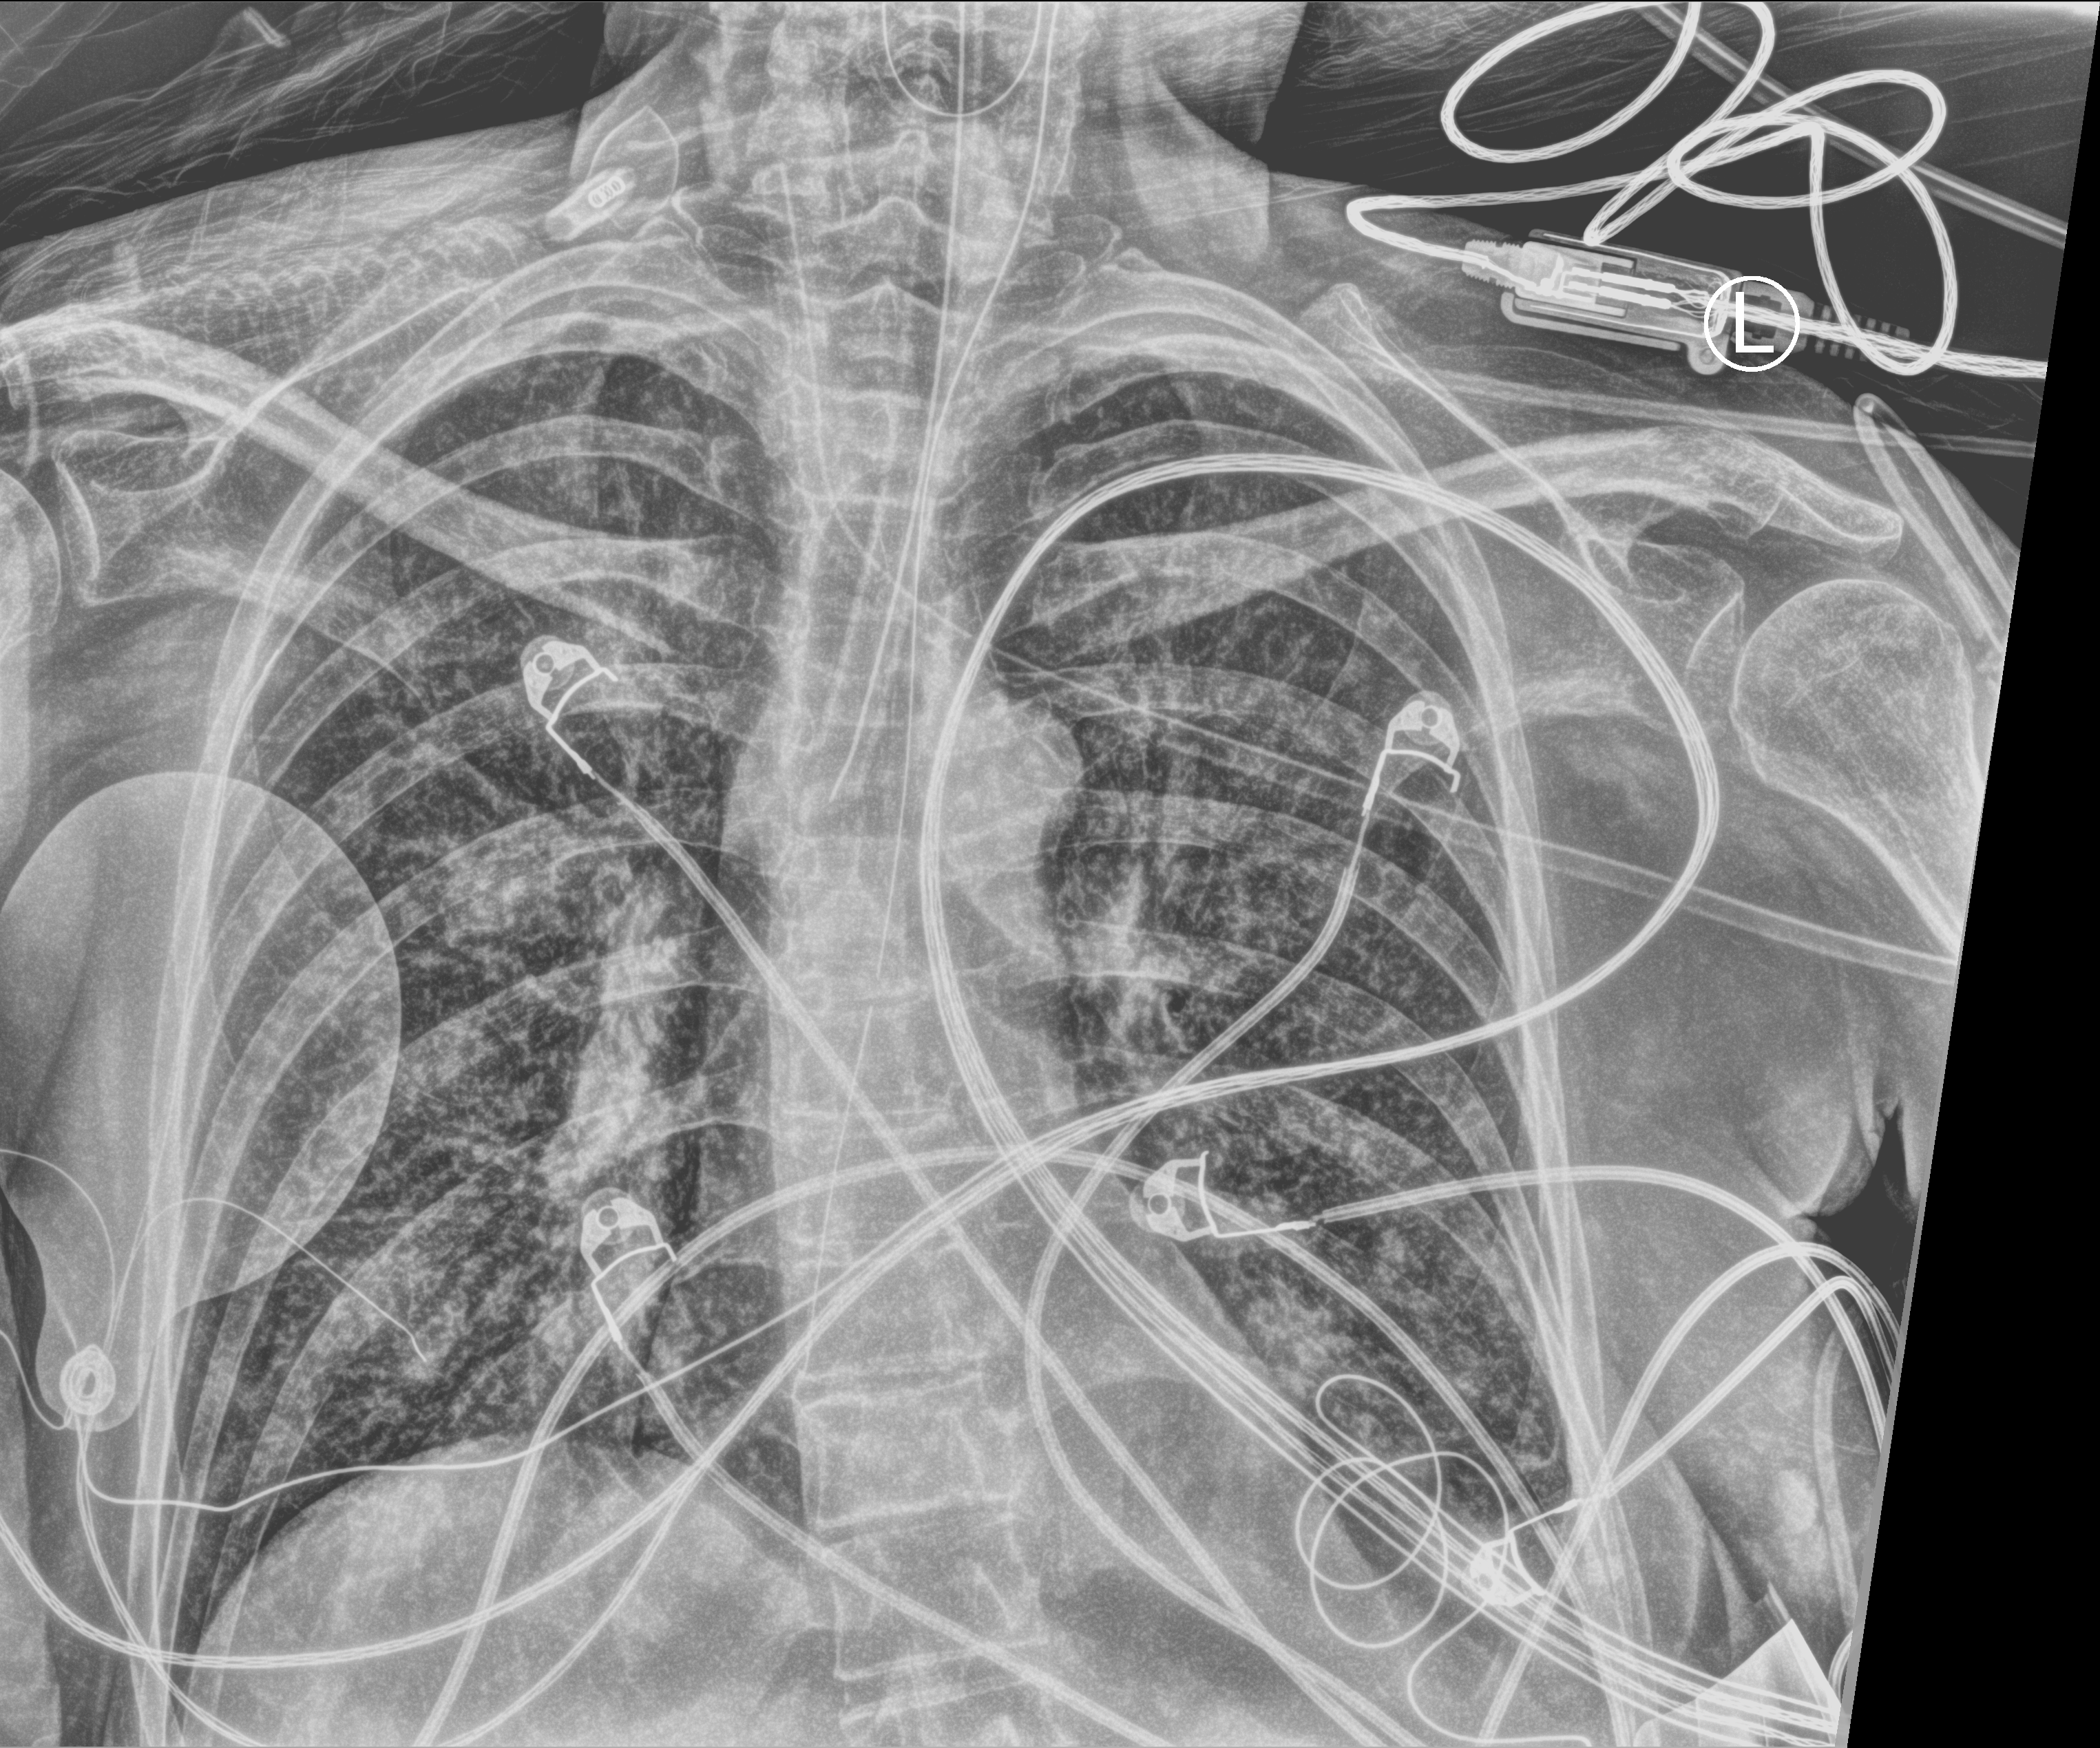
Bedside chest radiograph (computed radiography). Patient hospitalised with COVID-19, aged 18–59 years.
From the hospital-stay record, not from the radiograph (when in the stay this image was taken is not recorded): admitted to intensive care during this hospital stay: yes; smoking status (admission record): never; mechanically ventilated during this hospital stay: yes.